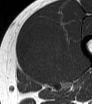
MRI of an extremity soft-tissue mass, one axial slice; slice 26 of 62 in the series (ordered by position); MR volume resampled by the dataset authors to the PET/CT grid (not the native acquisition matrix); 3.27 mm slice thickness; 92 × 104 image matrix, field of view 90 × 102 mm. Male patient. Case-level facts recorded for this patient, not image findings: histological type: mixoid liposarcoma; grade: low; site of the primary tumour: left thigh.
Annotated regions visible in this slice (expert contour drawn on MRI and transferred to this co-registered scan by the dataset authors):
- gross tumour volume (mass): box from (x=19, y=22) to (x=67, y=82) px